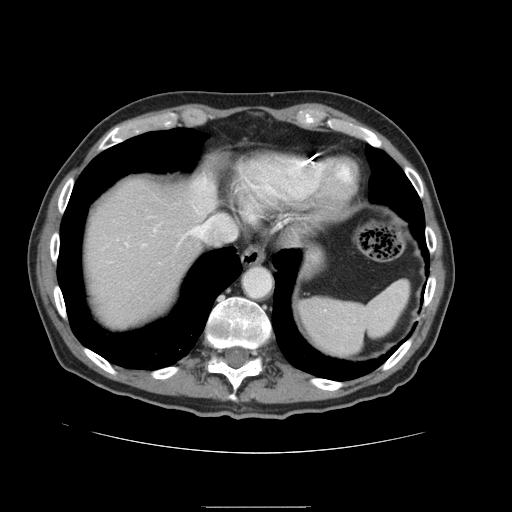
Contrast-enhanced abdominal CT, one axial slice. Slice 131 of 168 in the series (ordered by position). 120 kVp. Intravenous contrast given. Soft-tissue window (W 400 / L 40 HU). 2.5 mm slice thickness. 512 × 512 image matrix, field of view 386 × 386 mm. Male patient, age 74 years. From the clinical record (not read from this slice): diagnosis: colorectal cancer liver metastases, imaged before liver resection.
Annotated regions visible in this slice (manually delineated by an expert):
- liver: bounding box (x1, y1, x2, y2) in pixels: (83, 174, 218, 330)
- planned liver remnant (the part of the liver to remain after resection): (83, 173, 219, 330)